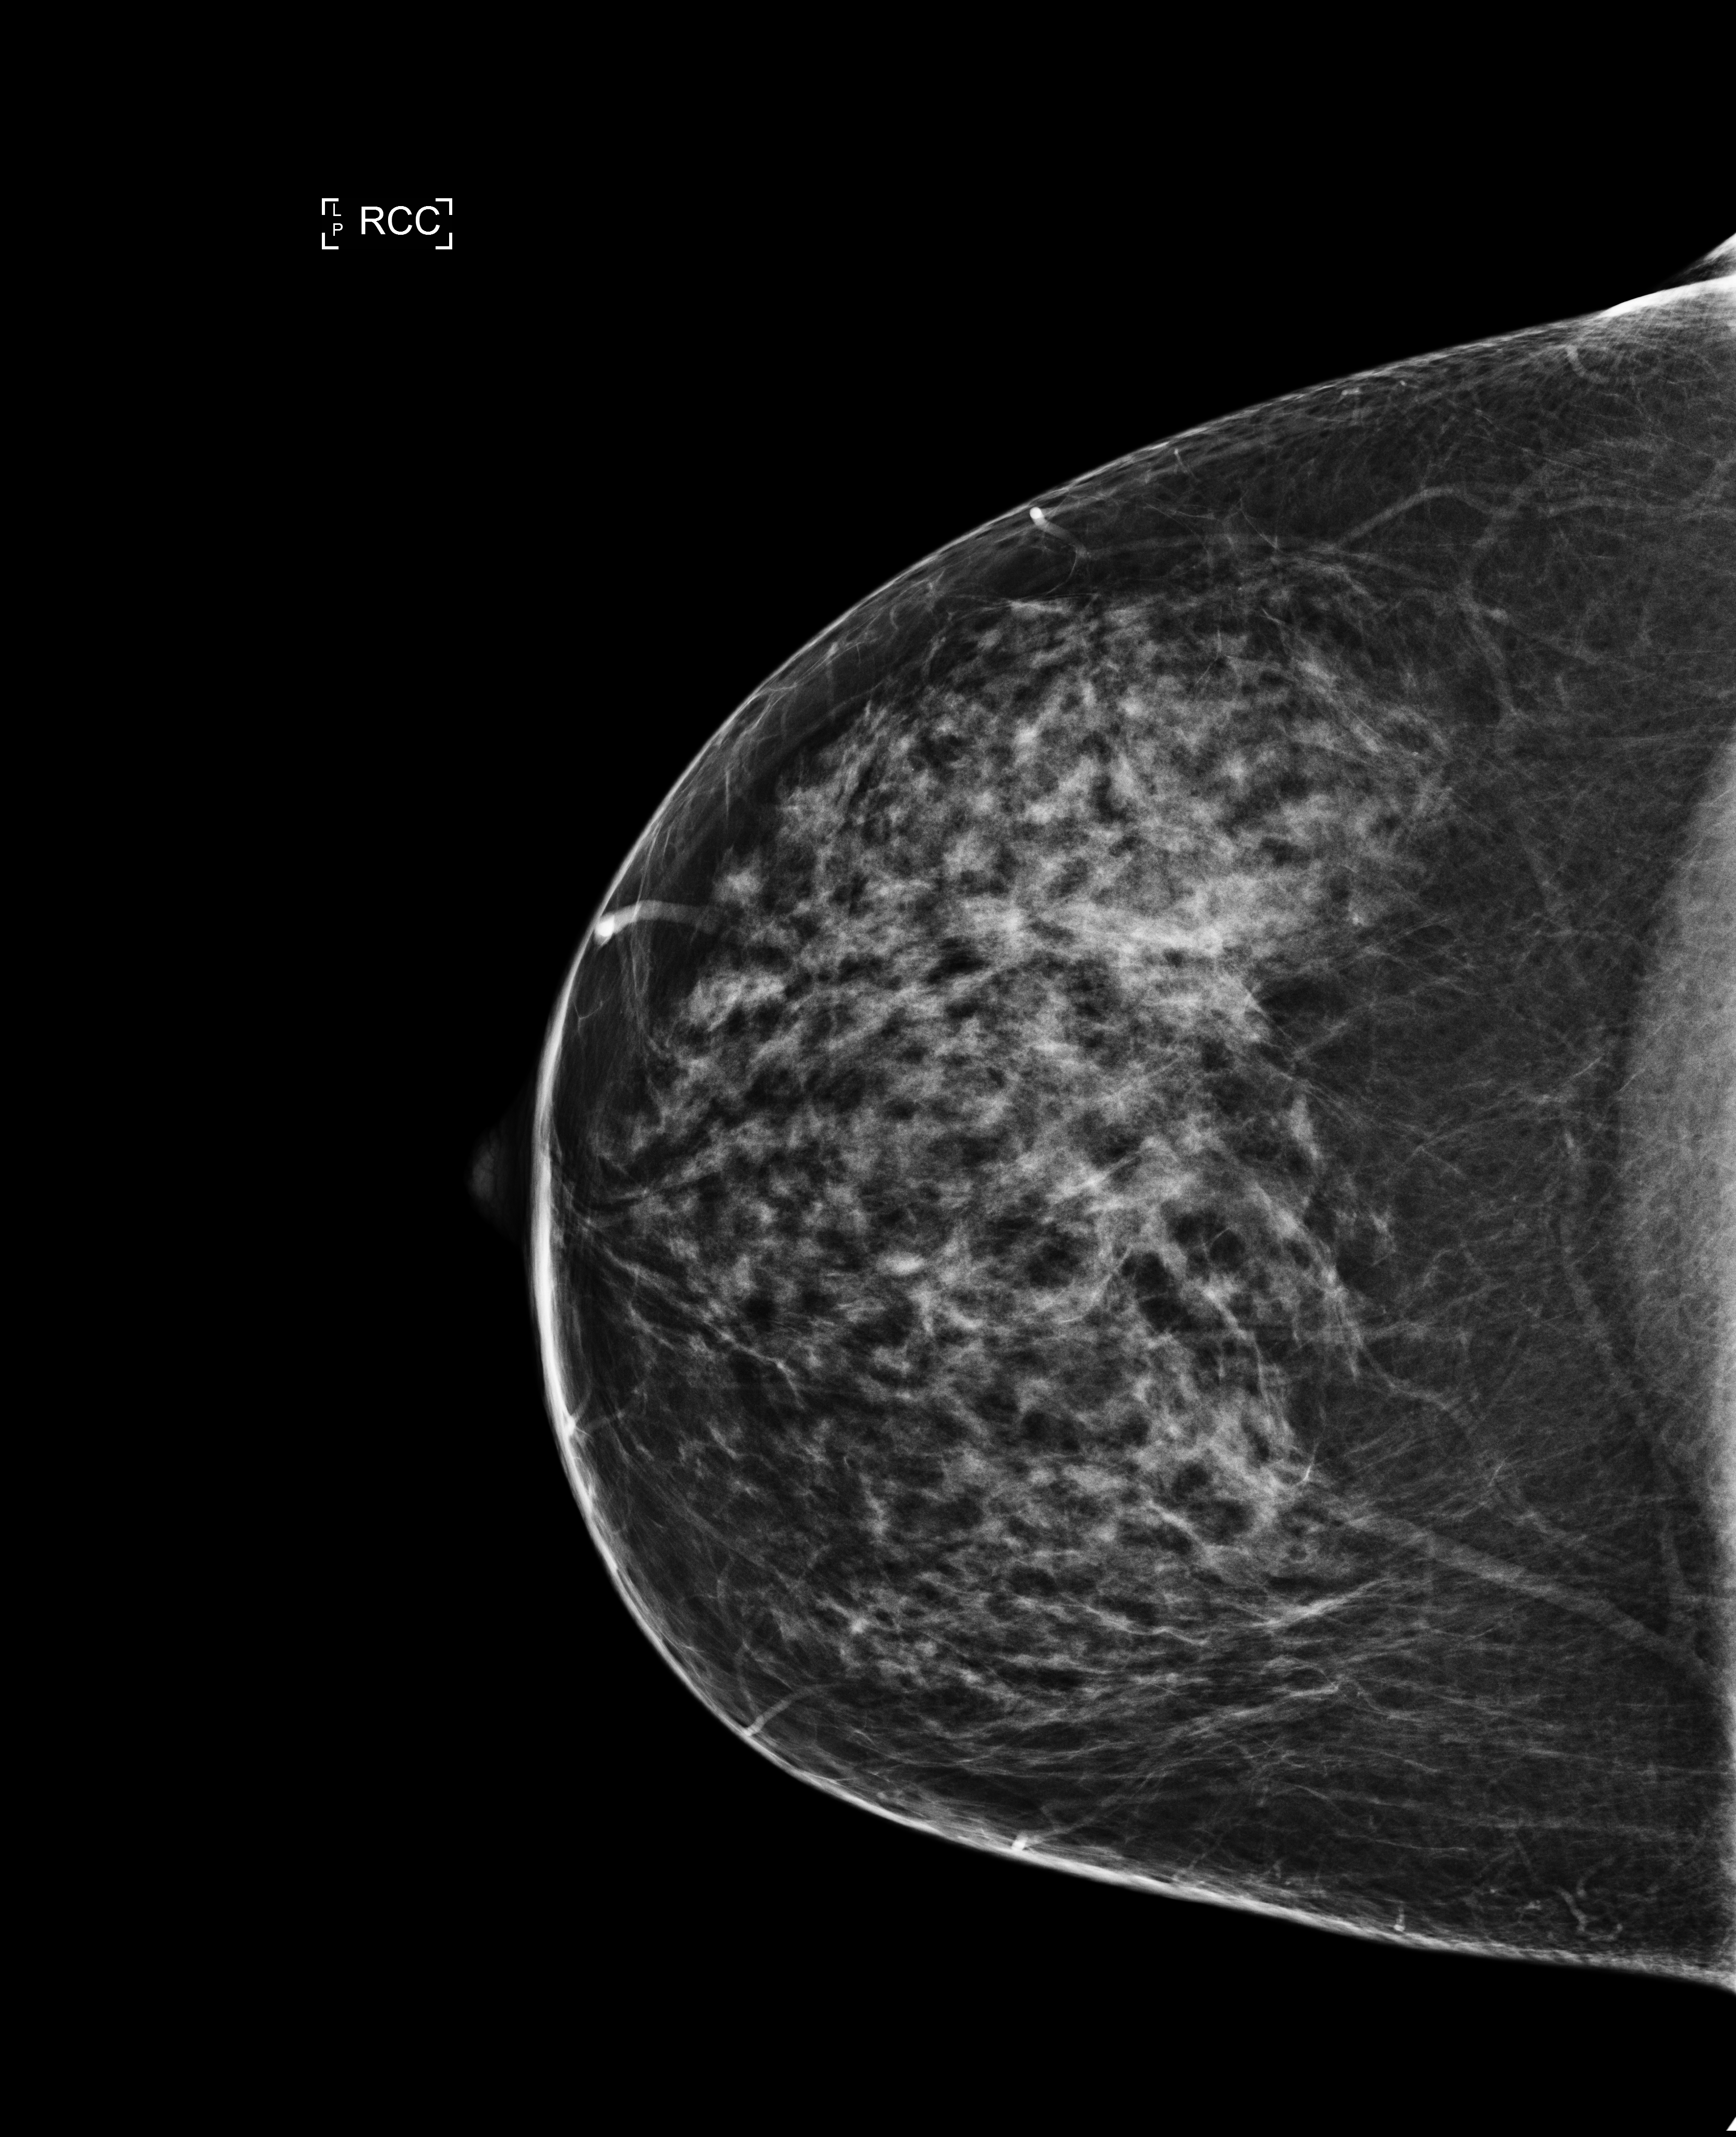
Screening examination. Female patient, age 50 years.
Image type: full-field digital mammogram. Breast: right. Projection: cranio-caudal projection. BI-RADS breast density category at the screening exam (both breasts, scale 1–4): 3. Final BI-RADS category for the screening round (tomosynthesis exam, both breasts): category 1. Recall: no recall after this screen.